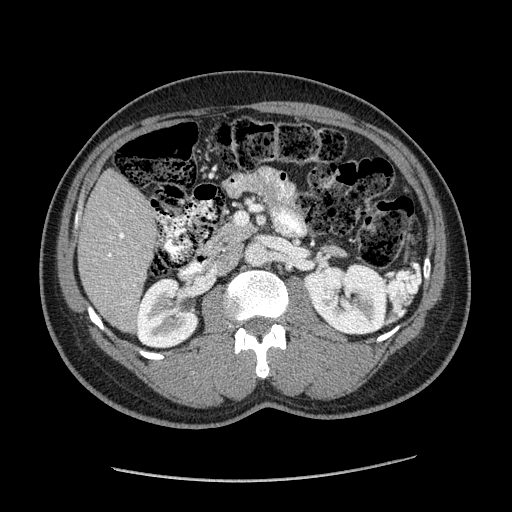
Contrast-enhanced abdominal CT (liver protocol), one axial slice. Slice 67 of 182 in the series (ordered by position). Reconstruction kernel STANDARD. Soft-tissue window (W 400 / L 40 HU). 2.5 mm slice thickness. 512 × 512 image matrix, field of view 400 × 400 mm. From the clinical record (not read from this slice): diagnosis: hepatocellular carcinoma (patient treated with transarterial chemoembolisation; whether this scan precedes or follows treatment is not stated here); TNM stage (as recorded): Stage-I; Child-Pugh class: A; tumour differentiation: well differentiated; tumour nodularity: uninodular.
Outlined on this slice (semi-automatic segmentation, software-assisted and operator-edited):
- liver parenchyma outside the tumour (the mass and vessels are separate outlines, so this box may not span the whole liver): bounding box [x1, y1, x2, y2] px = [78, 168, 156, 330]
- liver vessels: [109, 233, 124, 256]